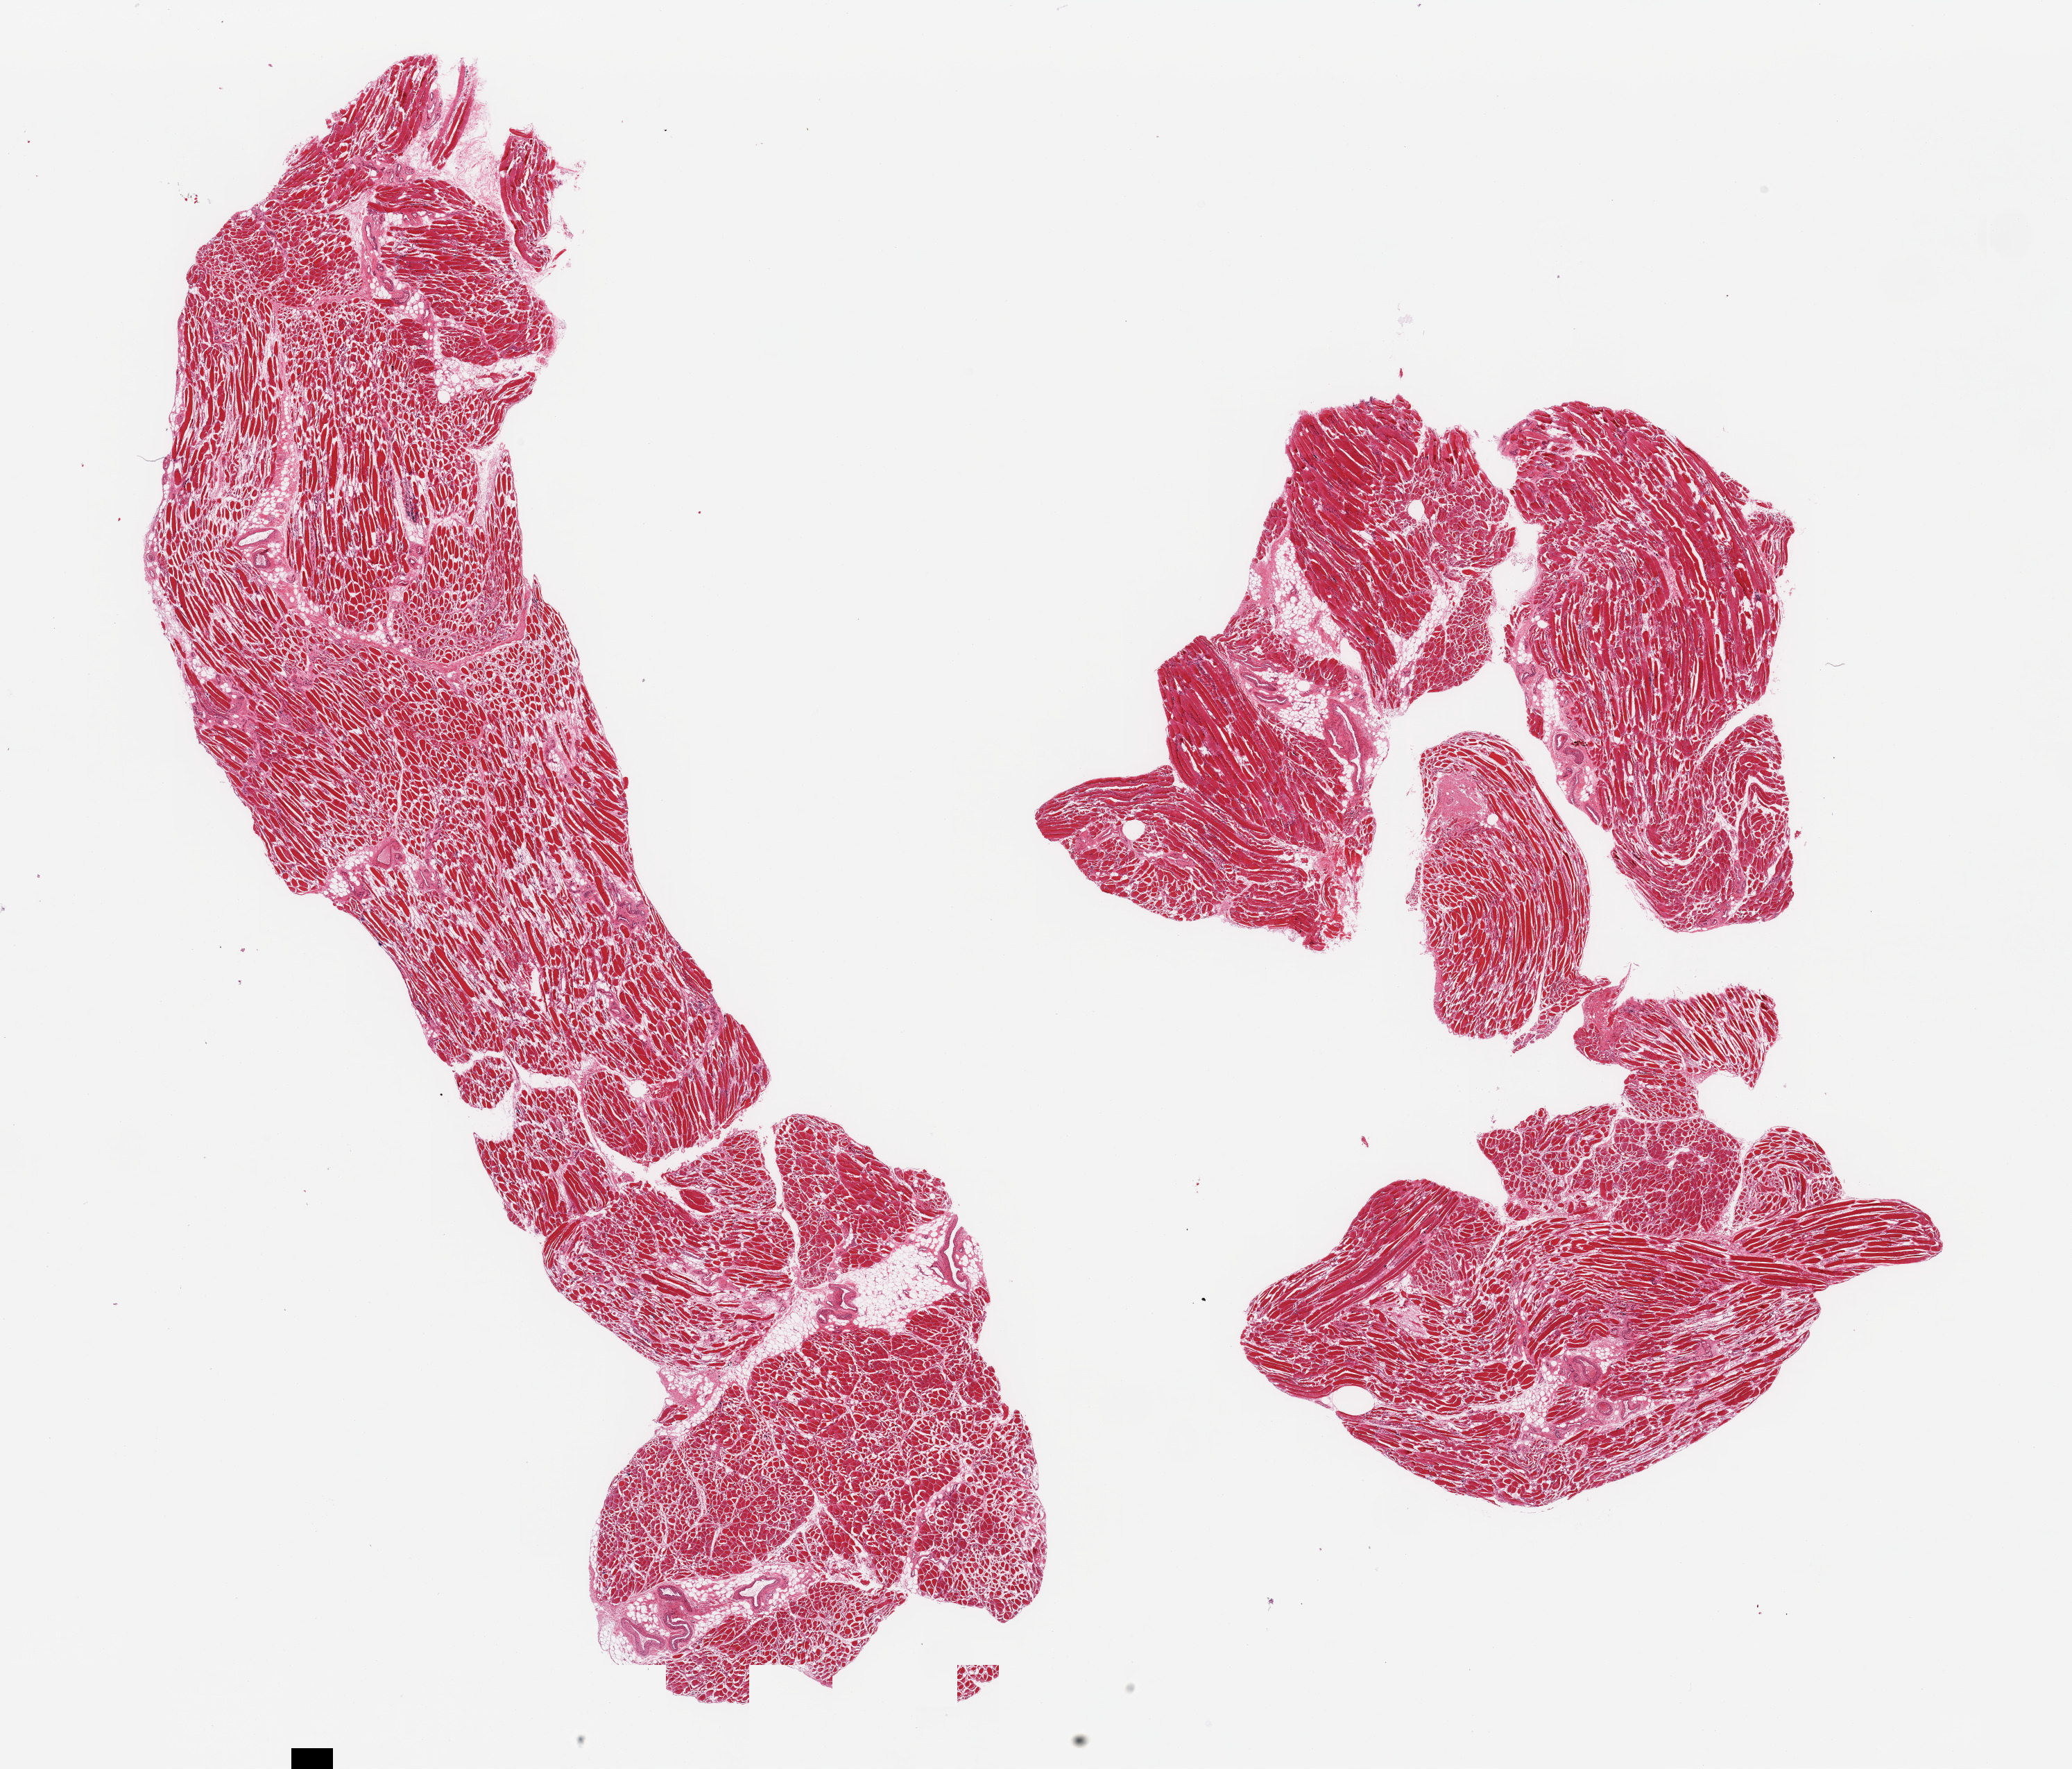
Haematoxylin and eosin whole-slide image, whole scanned area (about 23.6 x 20.2 mm, acquisition: 20x scan) shown as a low-resolution overview; PAXgene-fixed, paraffin-embedded tissue; section of skeletal muscle (target tissue); tissue donor sample. Donor: male.
• review note (as recorded): 2 pieces. Atrophic fibers, ~30-40% interstitial fat. Evidence of chronic myositis